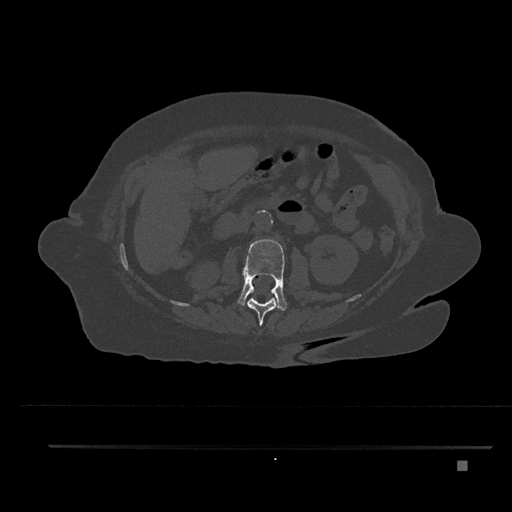
CT including the spine, one axial slice; position 194 of 797 along the scan axis; reconstruction kernel Br40s/3; 120 kVp; bone window (W 1800 / L 400 HU); 0.5 mm slice thickness; 512 × 512 image matrix, field of view 437 × 437 mm. Female patient, age 76 years. From the clinical record (not read from this slice): primary cancer: lung; vertebrae with lytic lesions (as recorded): T11, L3.
Structures marked on this image (semi-automatically segmented with operator editing):
- L1 vertebra: bounding box [x1, y1, x2, y2] px = [247, 298, 279, 326]
- L2 vertebra: [238, 239, 287, 311]